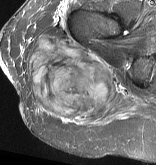
MRI of an extremity soft-tissue mass, one axial slice; position 31 of 57 along the scan axis; STIR; MR volume resampled by the dataset authors to the PET/CT grid (not the native acquisition matrix); 3.27 mm slice thickness; 156 × 165 image matrix, field of view 152 × 161 mm. Female patient. From the clinical record (not read from this slice): histological type: epithelioid sarcoma with vascular differentiation; site of the primary tumour: right buttock.
Annotated regions visible in this slice (expert contour drawn on MRI and transferred to this co-registered scan by the dataset authors):
- gross tumour volume (mass): bounding box <26,35,116,120> (left, top, right, bottom; pixels)